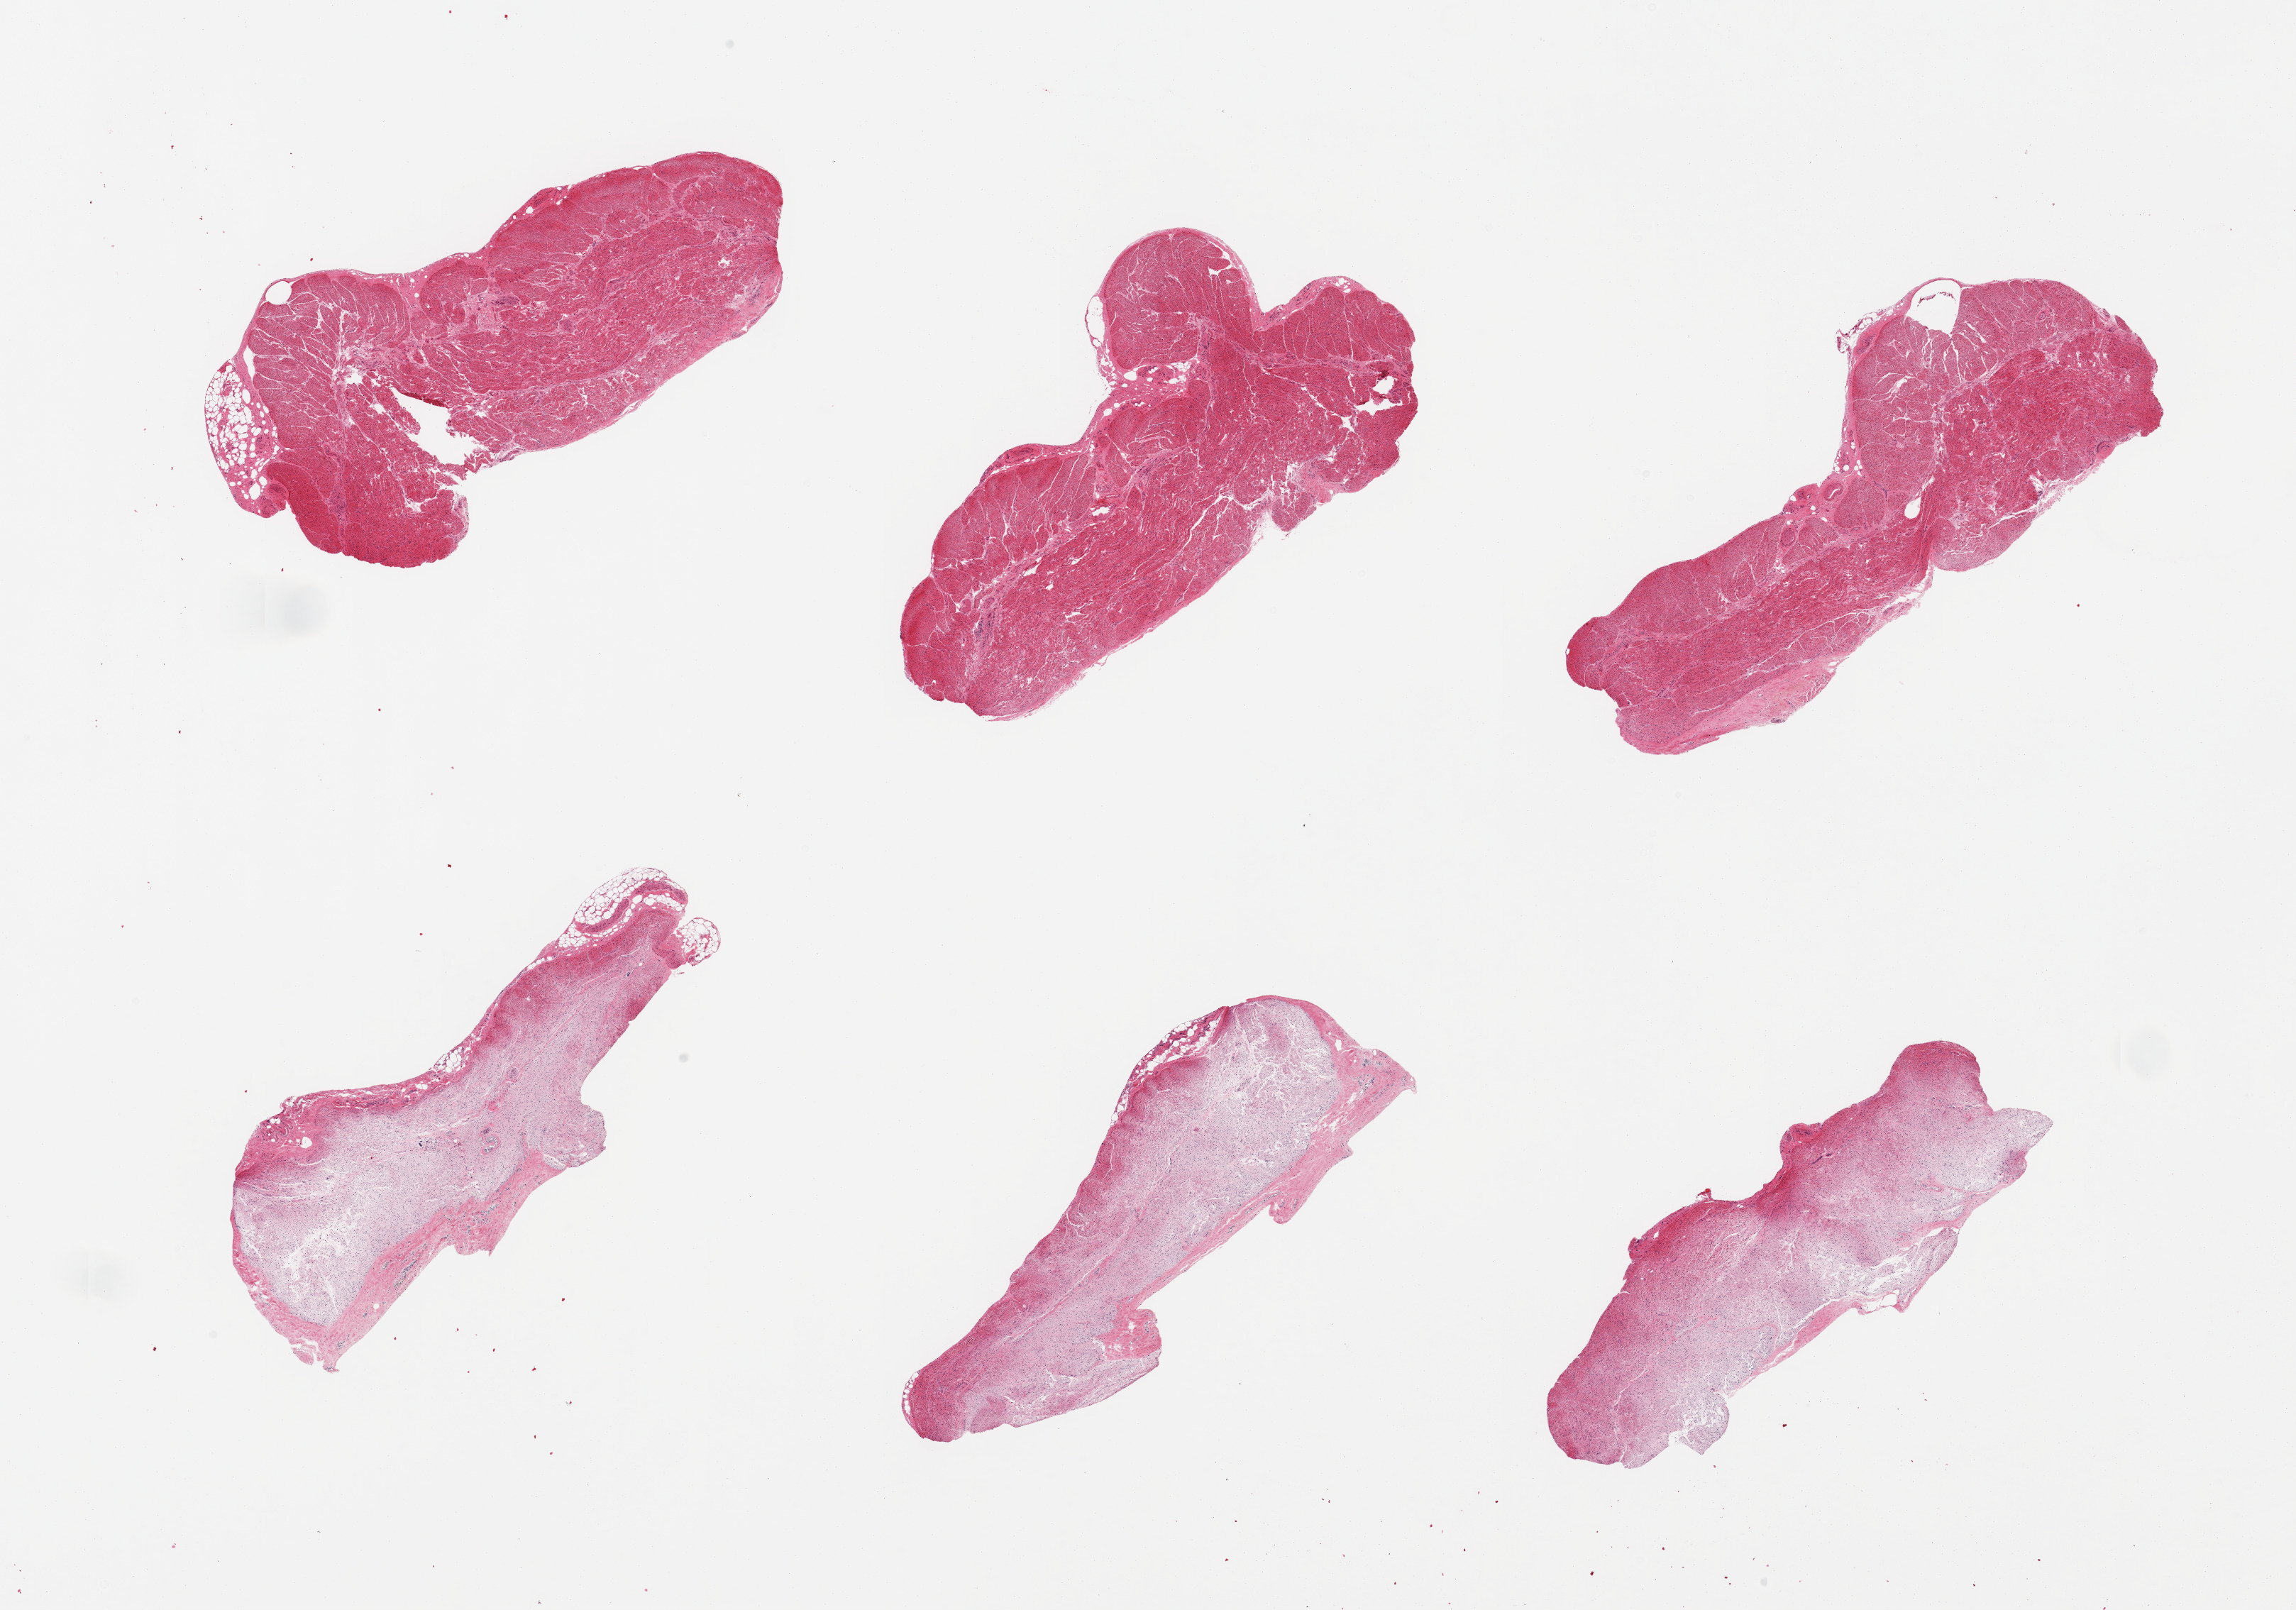
Whole-slide image, haematoxylin and eosin stain, brightfield, low-resolution overview of the scanned area, about 25.6 x 17.9 mm. PAXgene-fixed paraffin-embedded (PFPE) section. Sampled site (target tissue): esophageal muscle. Tissue donor sample. Donor: male.
- reviewer comment on this tissue sample: 6 pieces, unusally advanced autolysis